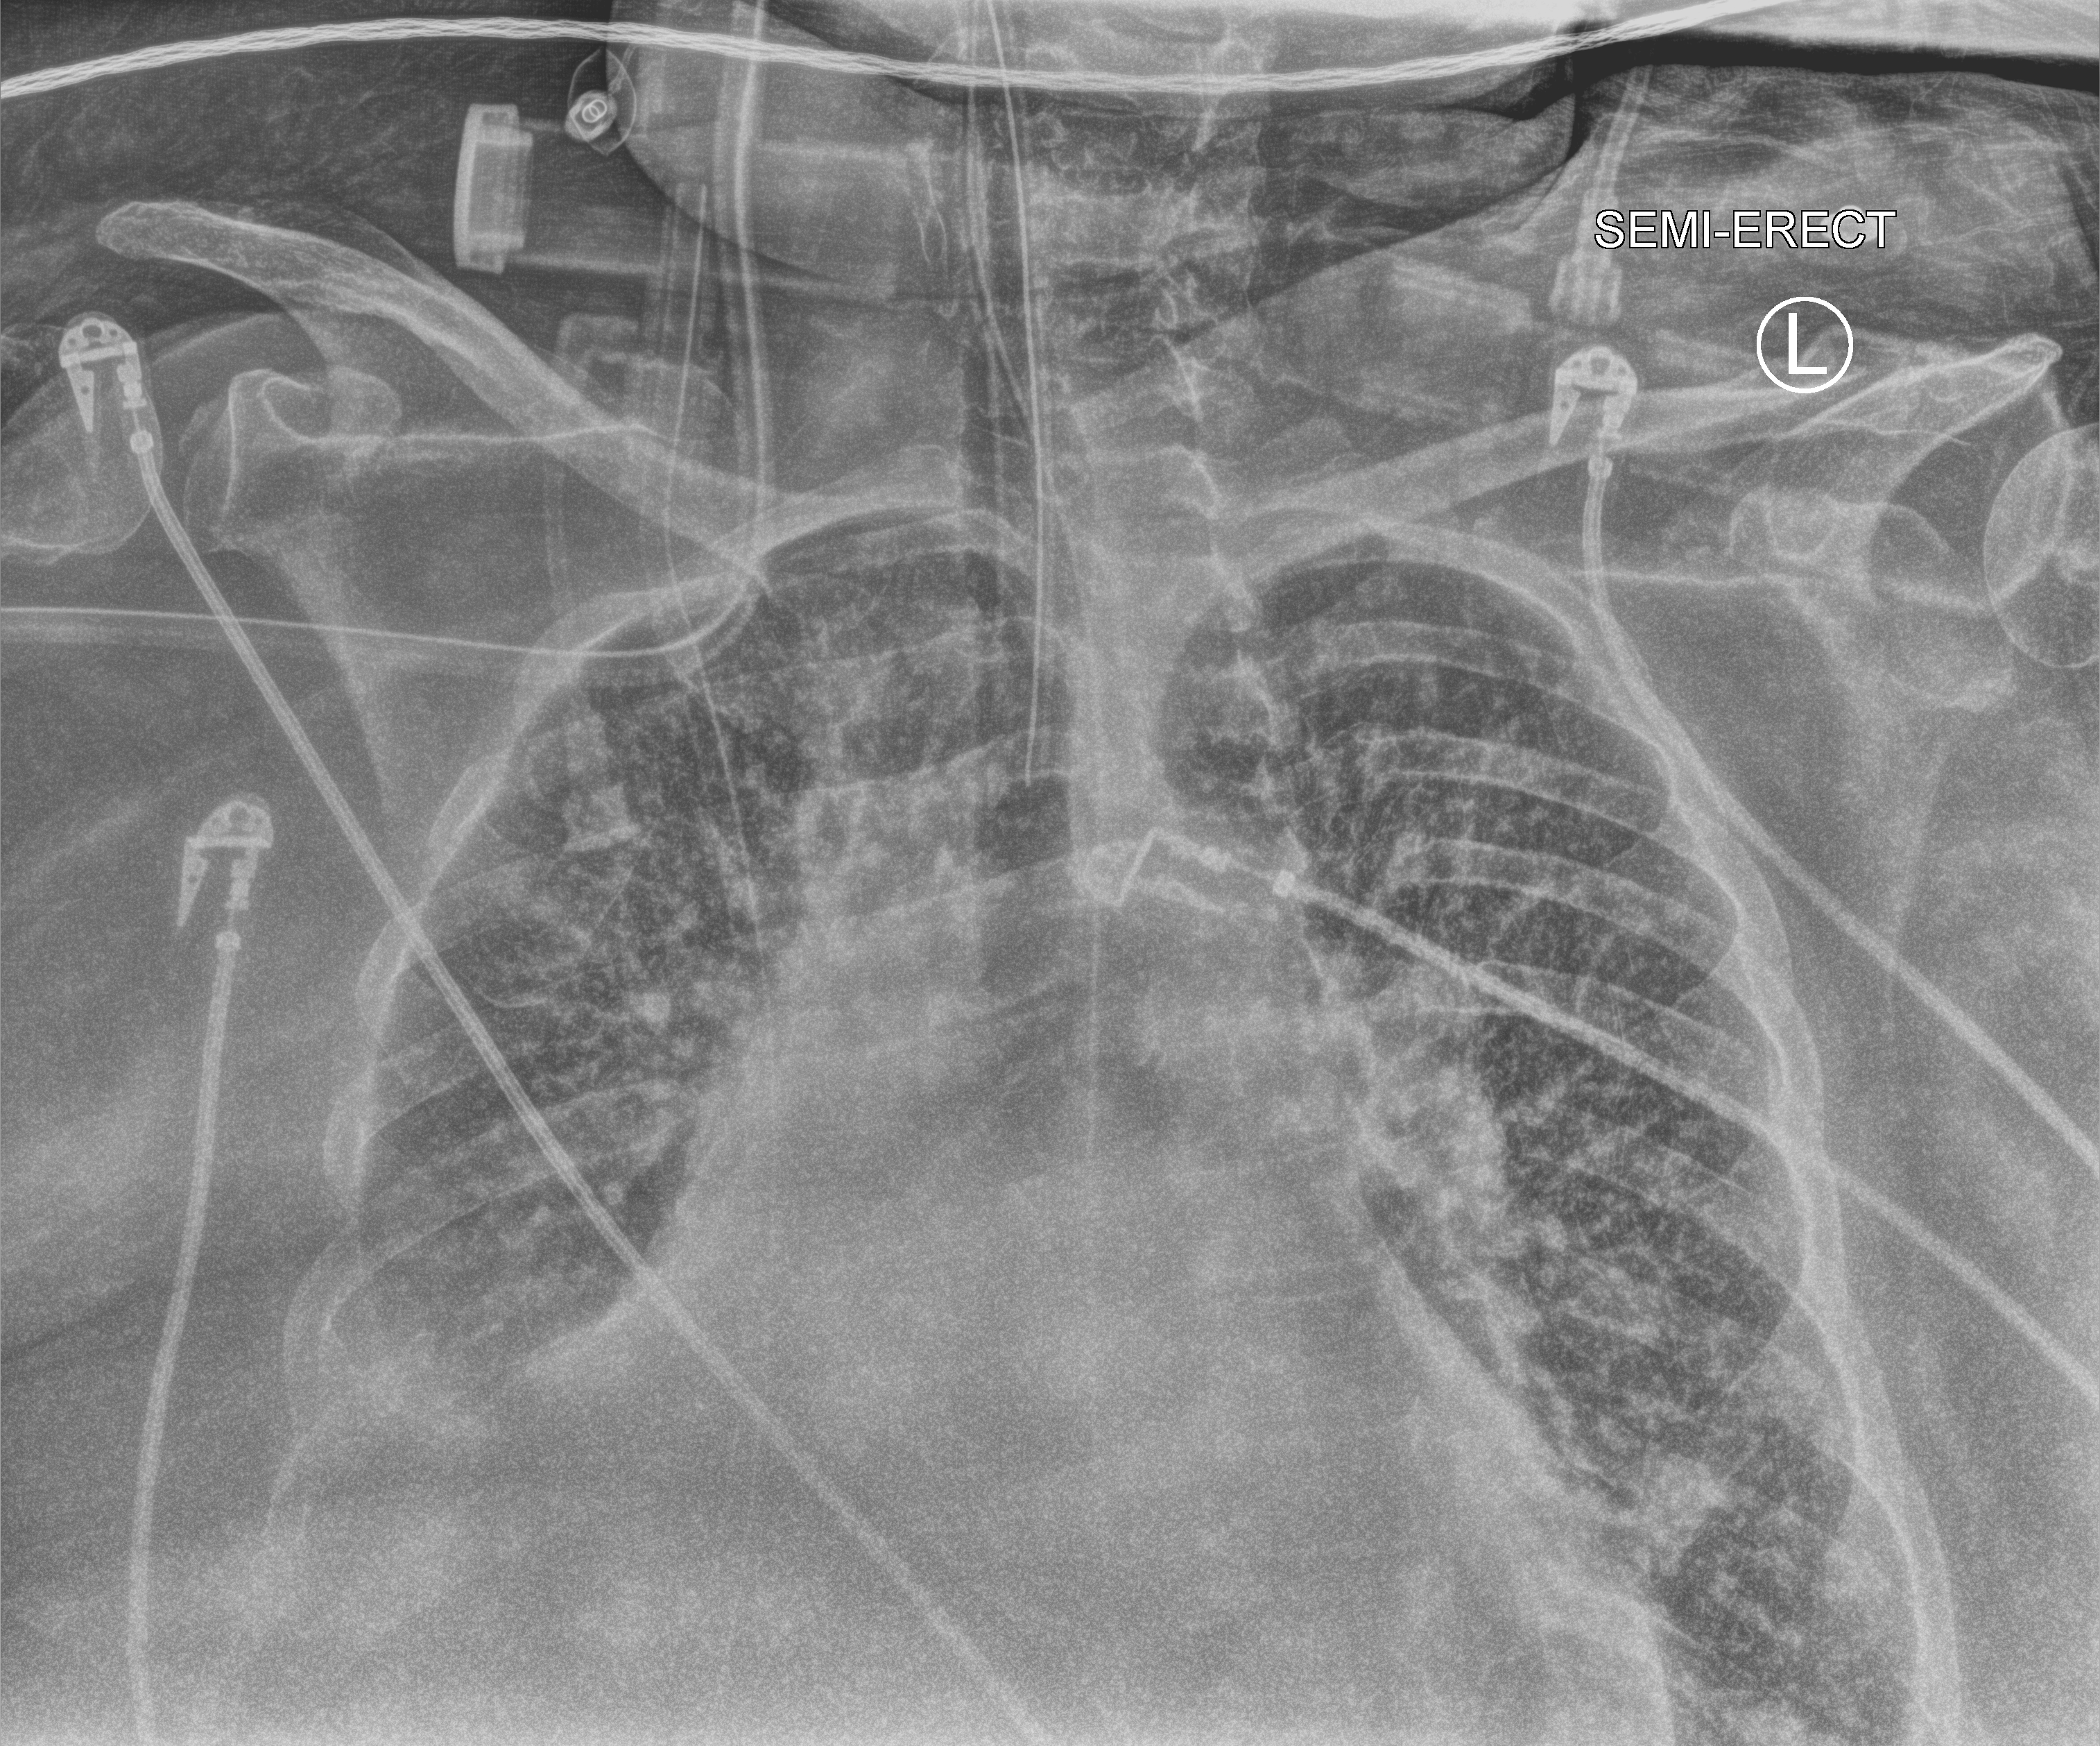
Bedside chest radiograph (computed radiography), anteroposterior (AP) projection. Patient hospitalised with COVID-19; female, aged 60–74 years.
From the hospital-stay record, not from the radiograph (when in the stay this image was taken is not recorded): COPD (admission record): yes; admitted to intensive care during this hospital stay: yes.